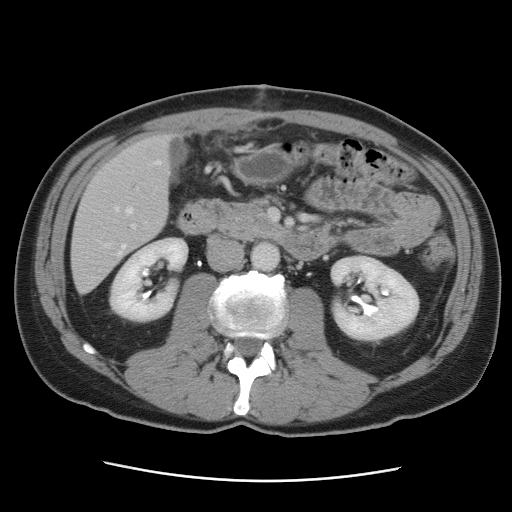
Contrast-enhanced abdominal CT, one axial slice; position 31 of 89 along the scan axis; 120 kVp; intravenous contrast given; soft-tissue window (W 400 / L 40 HU); 512 × 512 image matrix. Male patient, age 59 years. From the clinical record (not read from this slice): diagnosis: colorectal cancer liver metastases, imaged before liver resection; multiple liver metastases: yes; largest metastasis: 0.6 cm; disease in both lobes: yes.
Outlined on this slice (manually delineated by an expert):
- hepatic veins: bounding box (x1, y1, x2, y2) in pixels: (104, 161, 161, 257)
- liver: (73, 136, 170, 292)
- planned liver remnant (the part of the liver to remain after resection): (74, 135, 170, 245)
- portal vein (with intrahepatic branches): (132, 224, 135, 228)